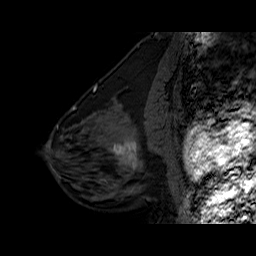
Breast MRI (dynamic contrast-enhanced), one sagittal slice; slice 25 of 60 in the series (ordered by position); dynamic contrast-enhanced series, time point 2 of 6 at this slice position (early post-contrast); 1.5 T; TE 6.3 ms, TR 32.5 ms; 4 mm slice thickness; 256 × 256 image matrix, field of view 200 × 200 mm. Female patient. From the clinical record (not read from this slice): setting: breast cancer imaged before/during neoadjuvant chemotherapy; receptor status: triple-negative.
Outlined on this slice (semi-automatic segmentation, software-assisted and operator-edited):
- analysis volume of interest (the breast-tissue region the enhancement analysis was run in; not a lesion): bounding box <102,127,162,186> (left, top, right, bottom; pixels)
- tumour enhancement mask (voxels above the 100 % enhancement threshold inside the analysis volume of interest): <113,140,141,171>